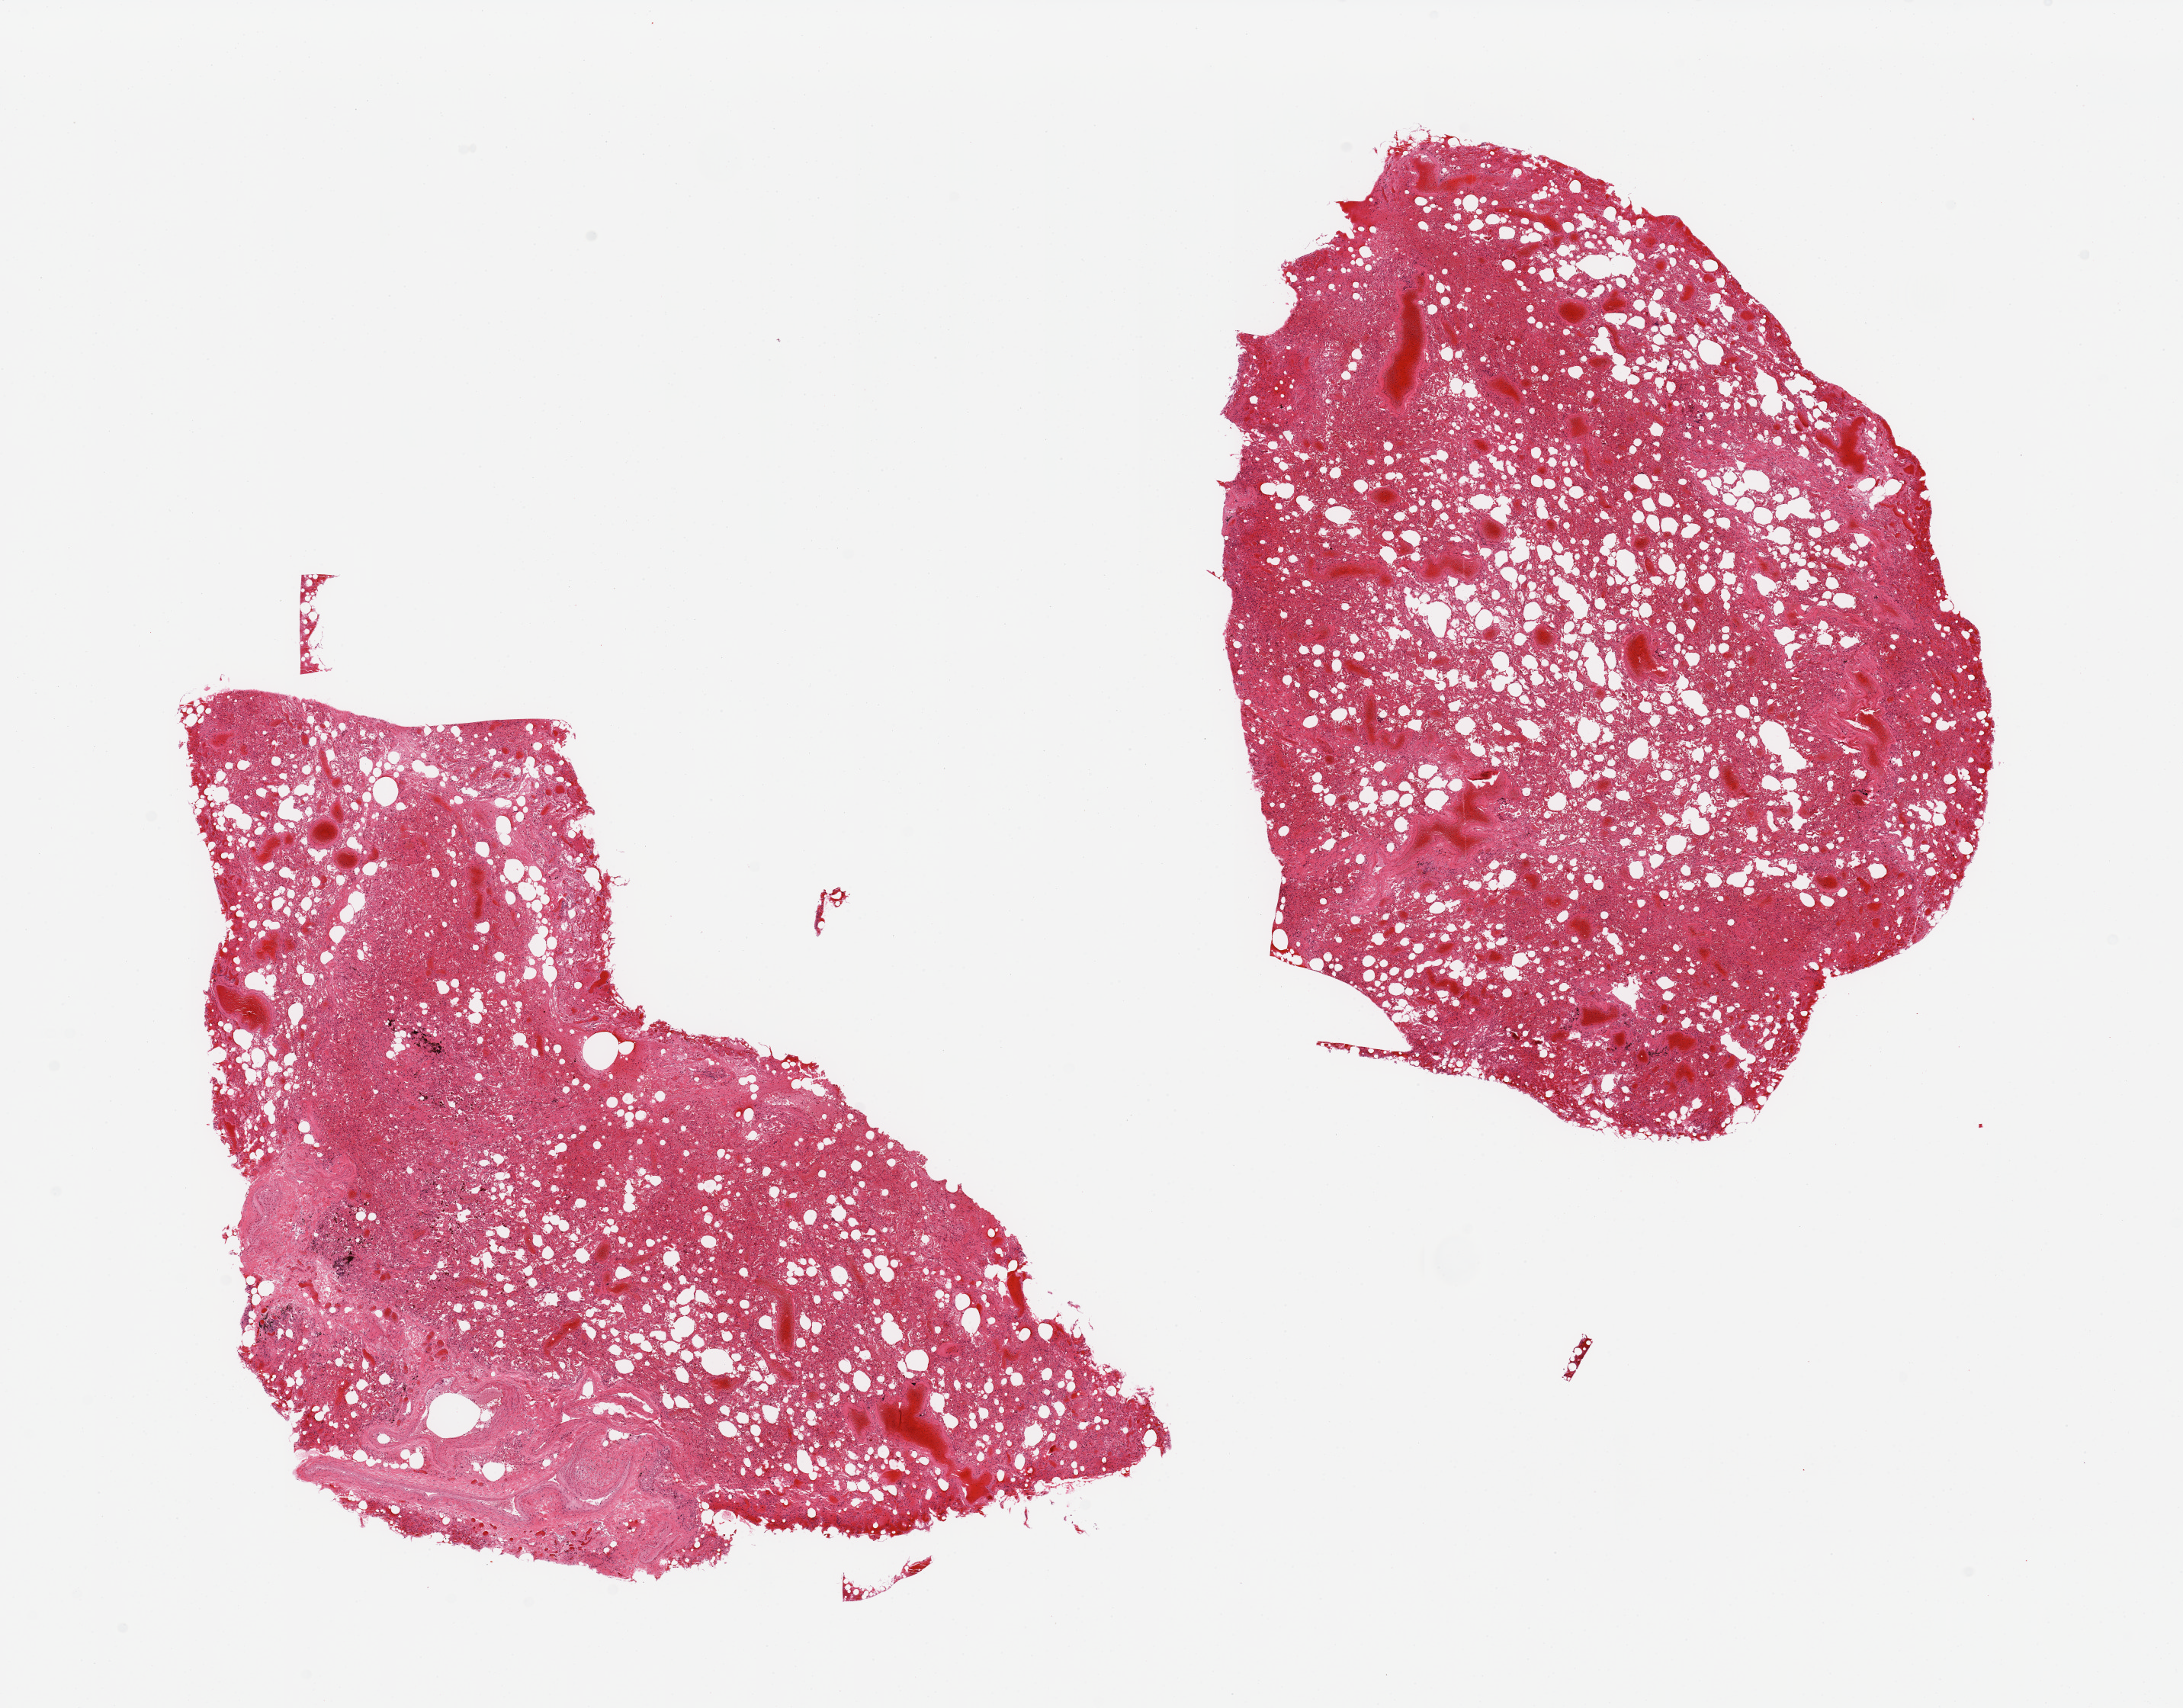
Whole-slide image, H&E stain — shown as a low-resolution overview of the whole scanned area (about 22.6 x 17.7 mm). PAXgene-fixed, paraffin-embedded tissue. Sampled site (target tissue): lung. Tissue donor sample.
• pathologist's review note for this sample: 2 pieces, marked congestion/hemorrhage